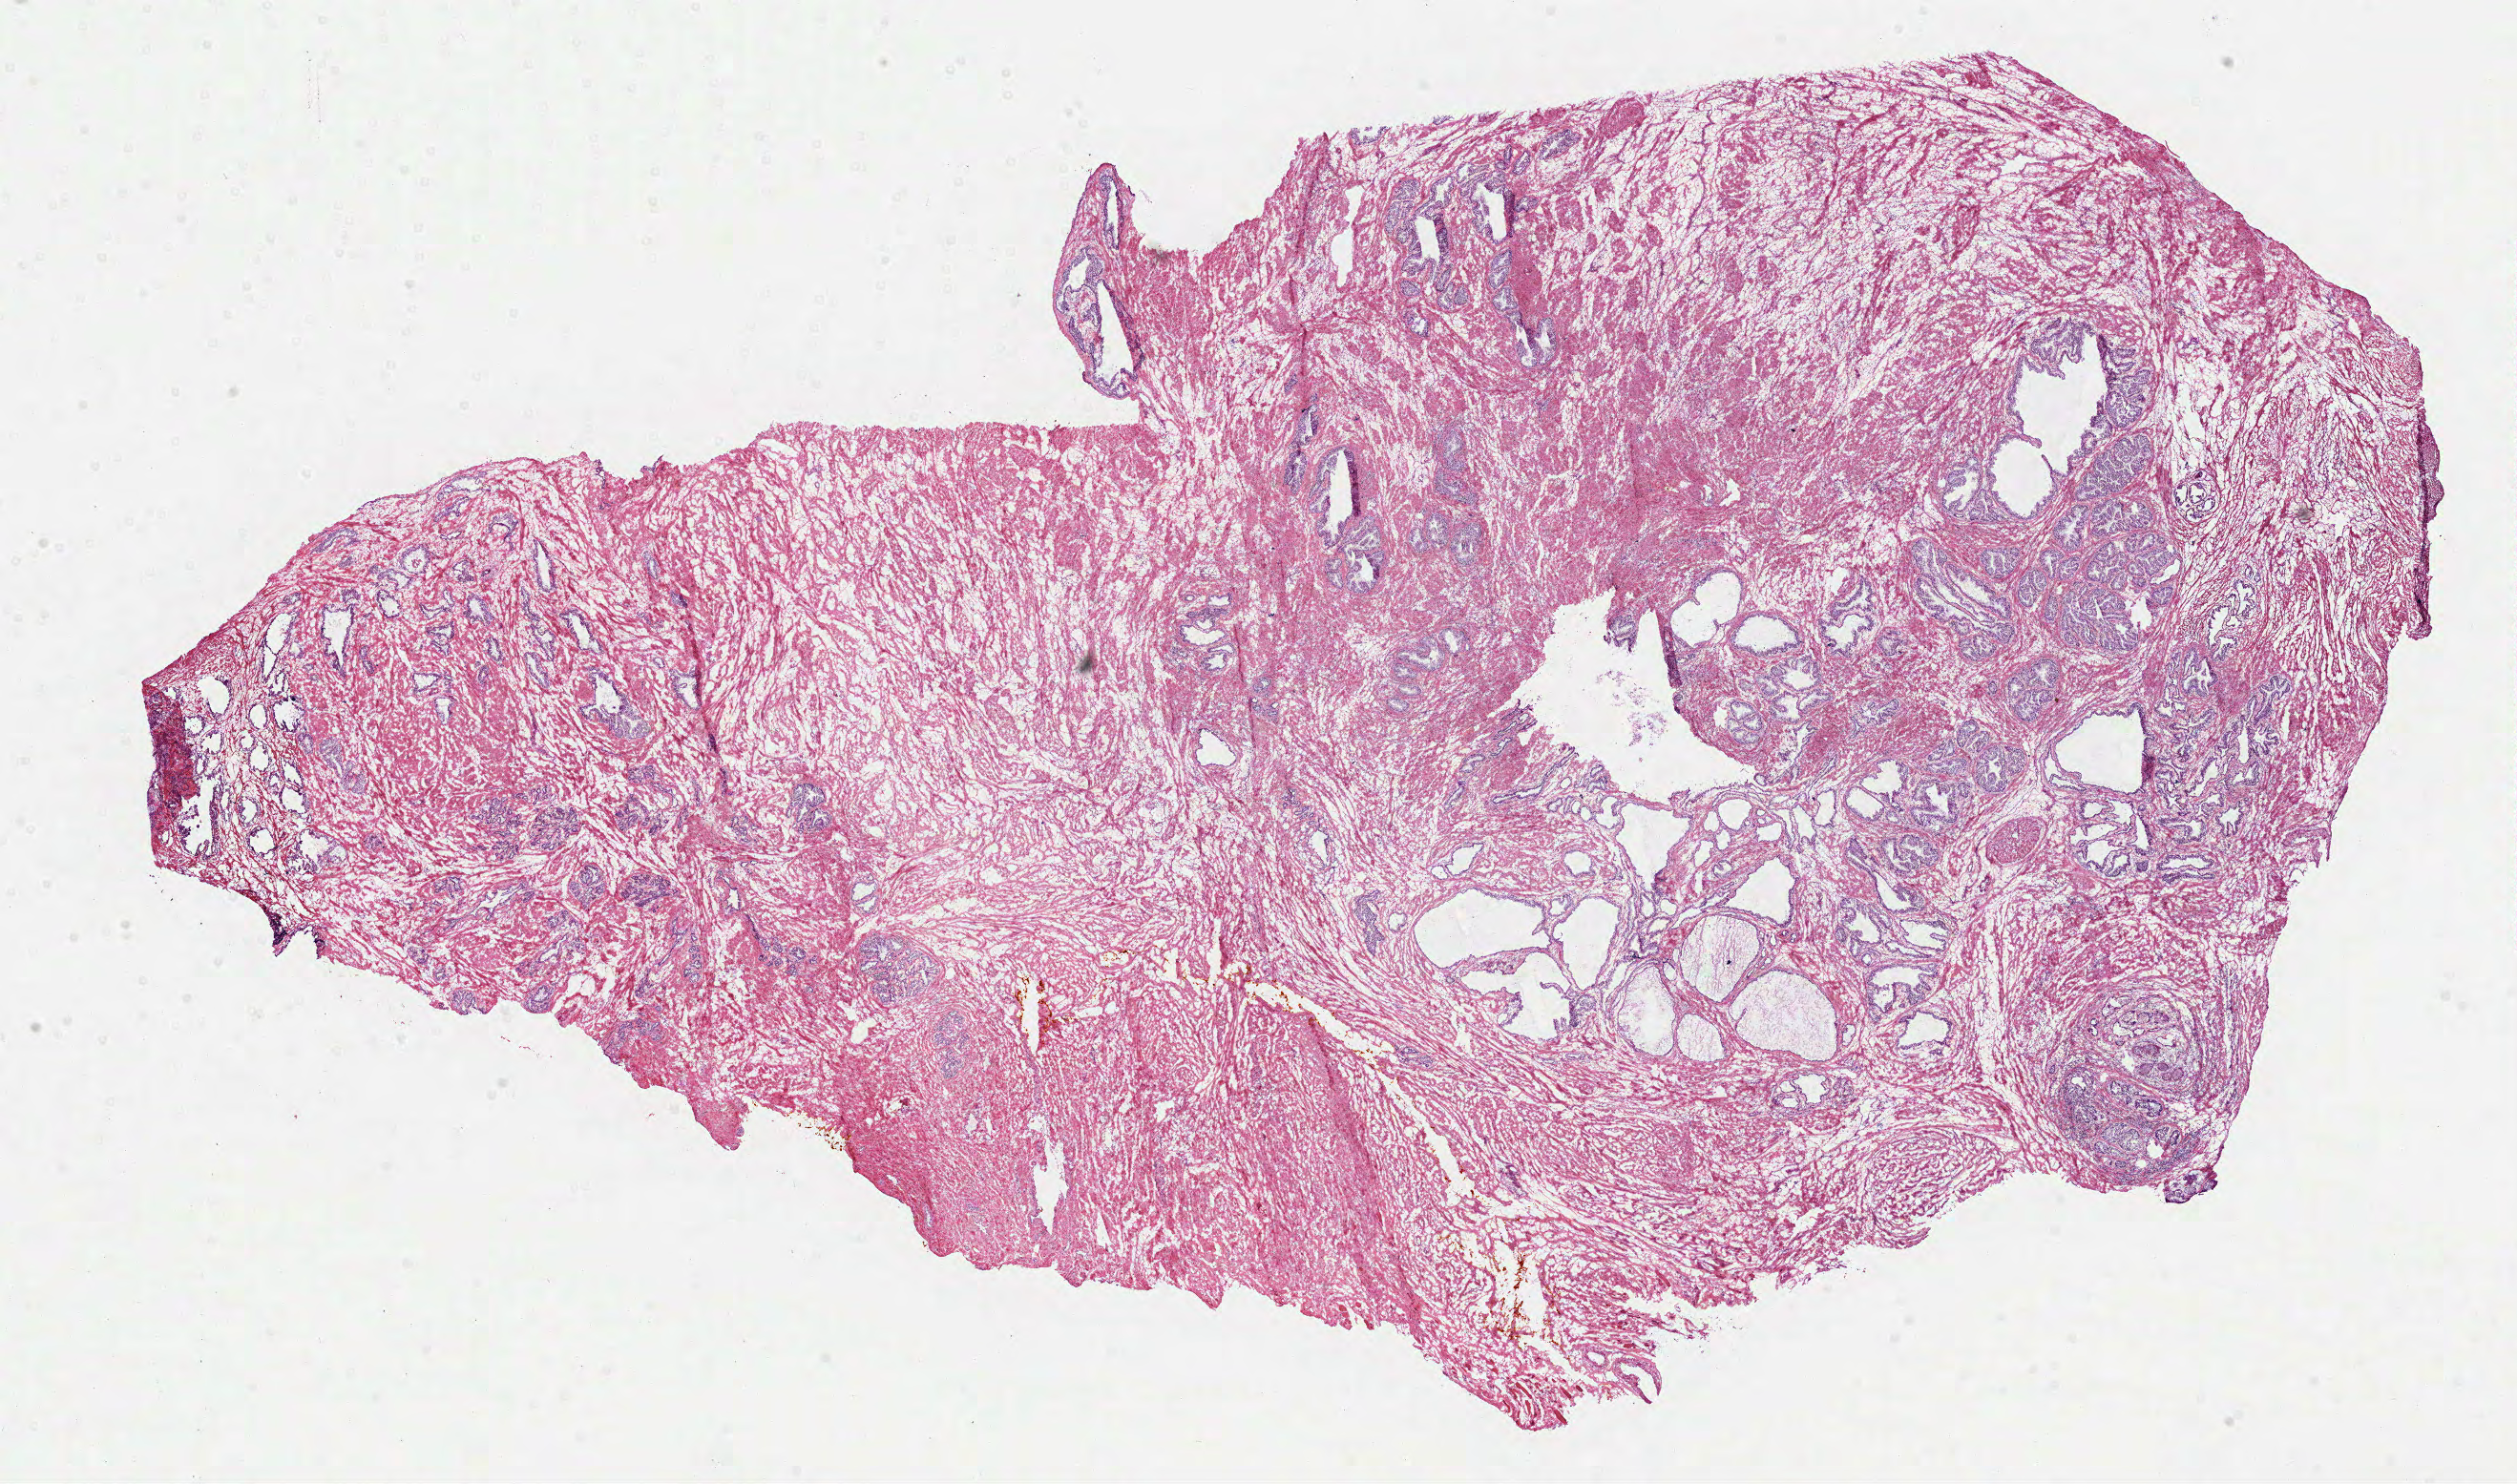
Whole-slide histology image, Hematoxylin and eosin (H&E) stained — whole scanned area (about 21.3 x 12.5 mm) shown as a low-resolution overview; frozen section from the top of the tissue portion; sample: solid tissue normal (non-tumour tissue), prostate. Patient: male, age at initial diagnosis 54 years.
* this section: solid tissue normal sample (biorepository sample class)
* patient diagnosis: Acinar cell carcinoma (prostate gland)